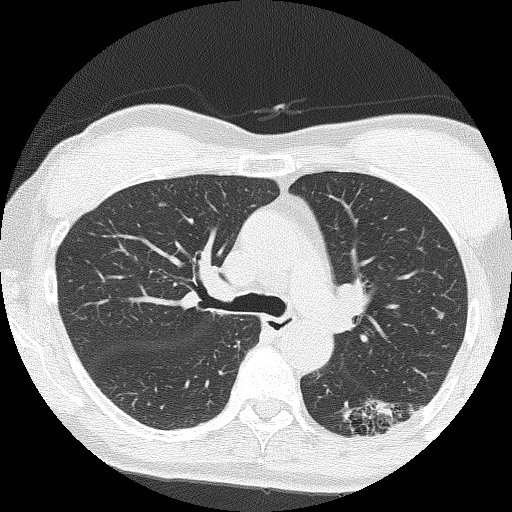
Chest CT (low-dose screening protocol), one axial image; second annual screen; lung window (W 1500 / L -600 HU); slice 57 of 159 in the series; 512 × 512 image matrix. Female, age 64 years at enrolment. Former smoker at enrolment.
Expert-annotated lung lesion, bounding box [x1, y1, x2, y2] px = [355, 387, 421, 440]. The screening reader recorded 3 non-calcified nodules or masses ≥4 mm on this exam (right upper lobe, right upper lobe, right middle lobe); which of them this box marks is not recorded. Later outcome: lung cancer diagnosed 576 days after this screen — adenocarcinoma, NOS, left lower lobe, moderately differentiated (G2), stage IA (AJCC 6th edition), 17 mm at pathology.